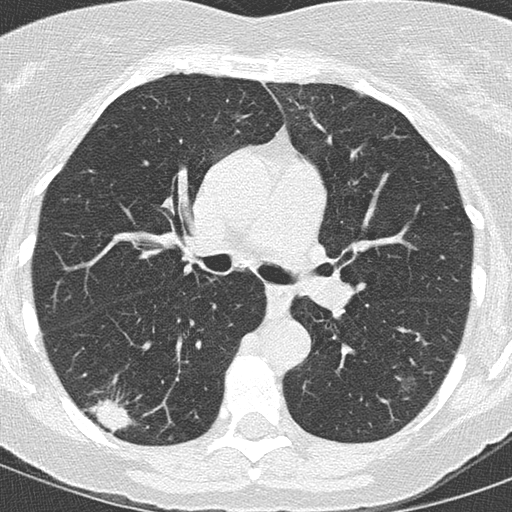
Axial slice from a low-dose chest CT screening exam, baseline screening round, lung window (W 1500 / L -600 HU), lung (sharp) reconstruction kernel (B50f). Female participant, aged 59 years at enrolment. Former smoker at enrolment.
• Expert reader's lesion annotation, bounding box [x1, y1, x2, y2] px = [69, 386, 146, 444].
• Screening reader's record for this exam (one nodule recorded; not confirmed to be the boxed lesion): non-calcified nodule or mass ≥4 mm, right lower lobe, 24 × 15 mm, spiculated (stellate) margins, soft tissue attenuation.
• Official screen result: positive, change unspecified: nodule(s) >= 4 mm or enlarging nodule(s), mass(es), or other non-specific abnormalities suspicious for lung cancer.
• Later outcome: lung cancer diagnosed 12 days after this screen — adenocarcinoma, NOS, right lower lobe, moderately differentiated (G2), stage IIB (AJCC 6th edition), 22 mm at pathology.